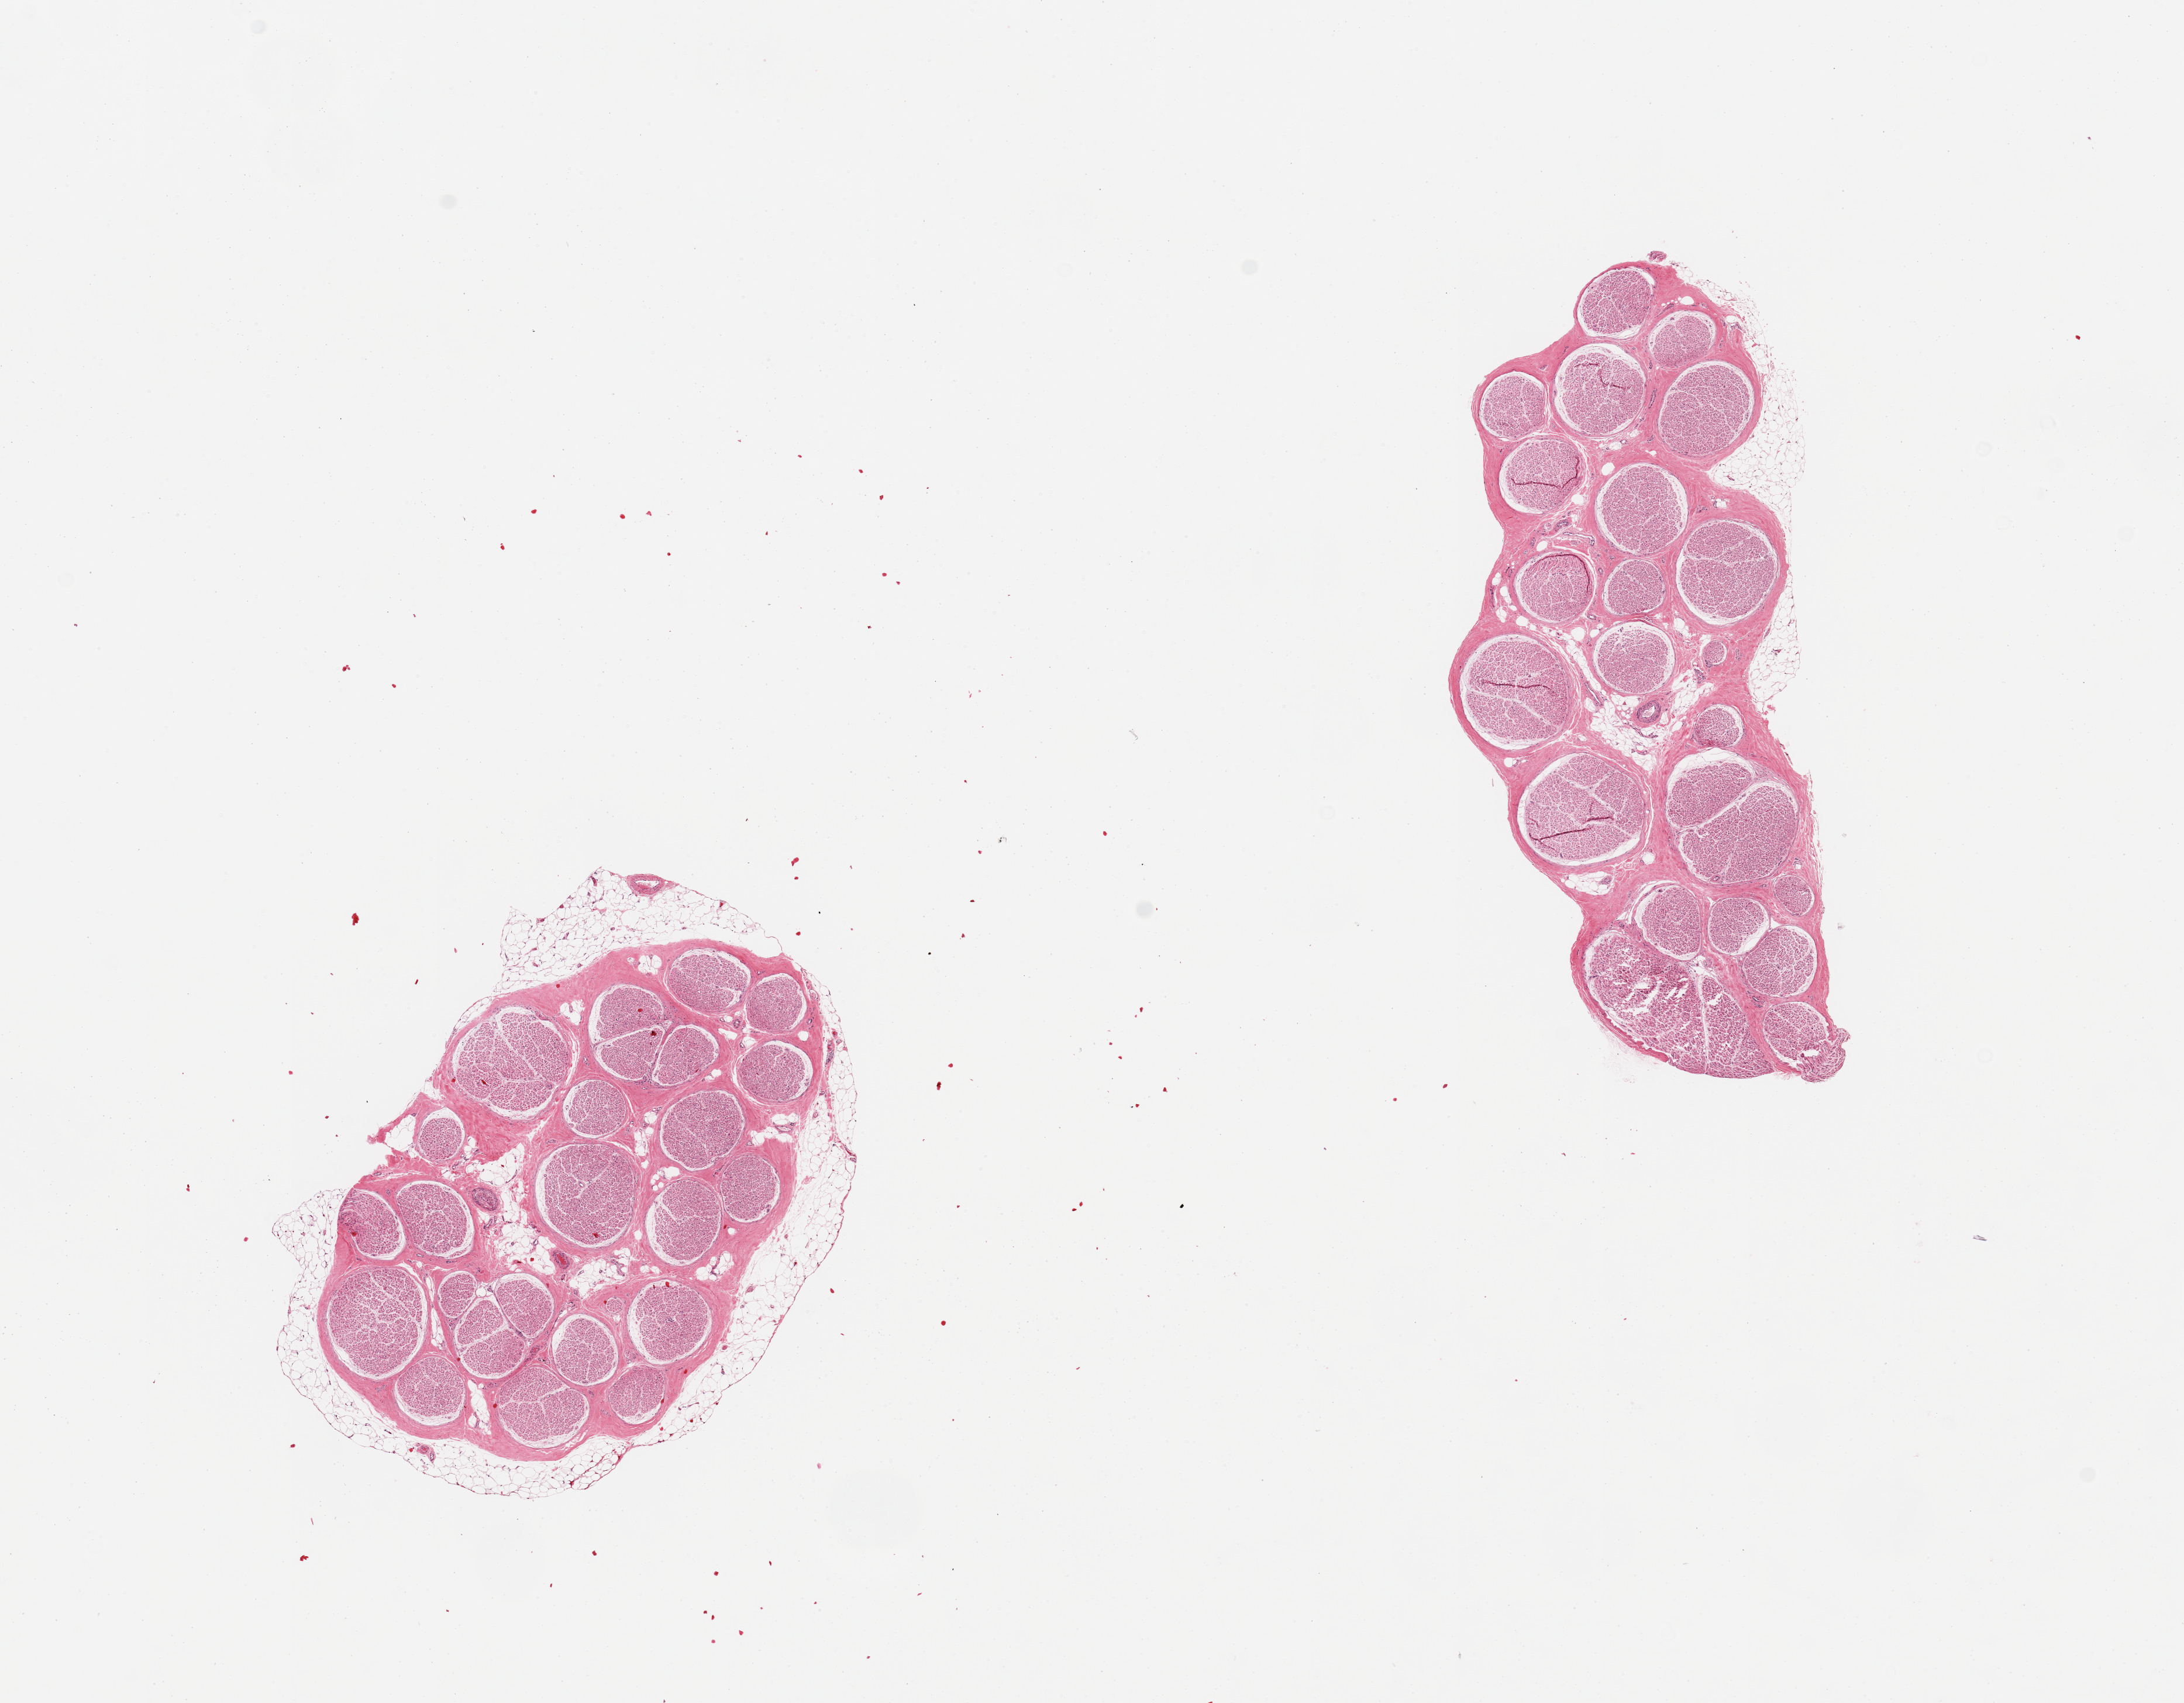
Digitized H&E-stained section, brightfield, low-resolution overview of the scanned area, about 14.8 x 11.5 mm (from a 20x scan), PAXgene-fixed paraffin-embedded (PFPE) section, sampled site (target tissue): tibial nerve, donor tissue sample. Donor: female.
* reviewer comment on this tissue sample: 2 pieces, both with small attachment of fat (5-10%)